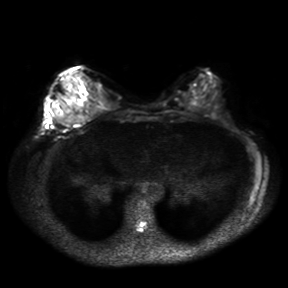
Breast MRI, one axial slice. Slice 13 of 30 in the series (ordered by position). Diffusion-weighted series; image 2 of 4 stored at this slice position (different b-values; order by instance number). 3 T. 4 mm slice thickness. 288 × 288 image matrix, field of view 360 × 360 mm. Female patient.
Annotated regions visible in this slice (manually delineated by an expert):
- tumour on diffusion-weighted imaging: bounding box [x1, y1, x2, y2] px = [54, 106, 62, 124]